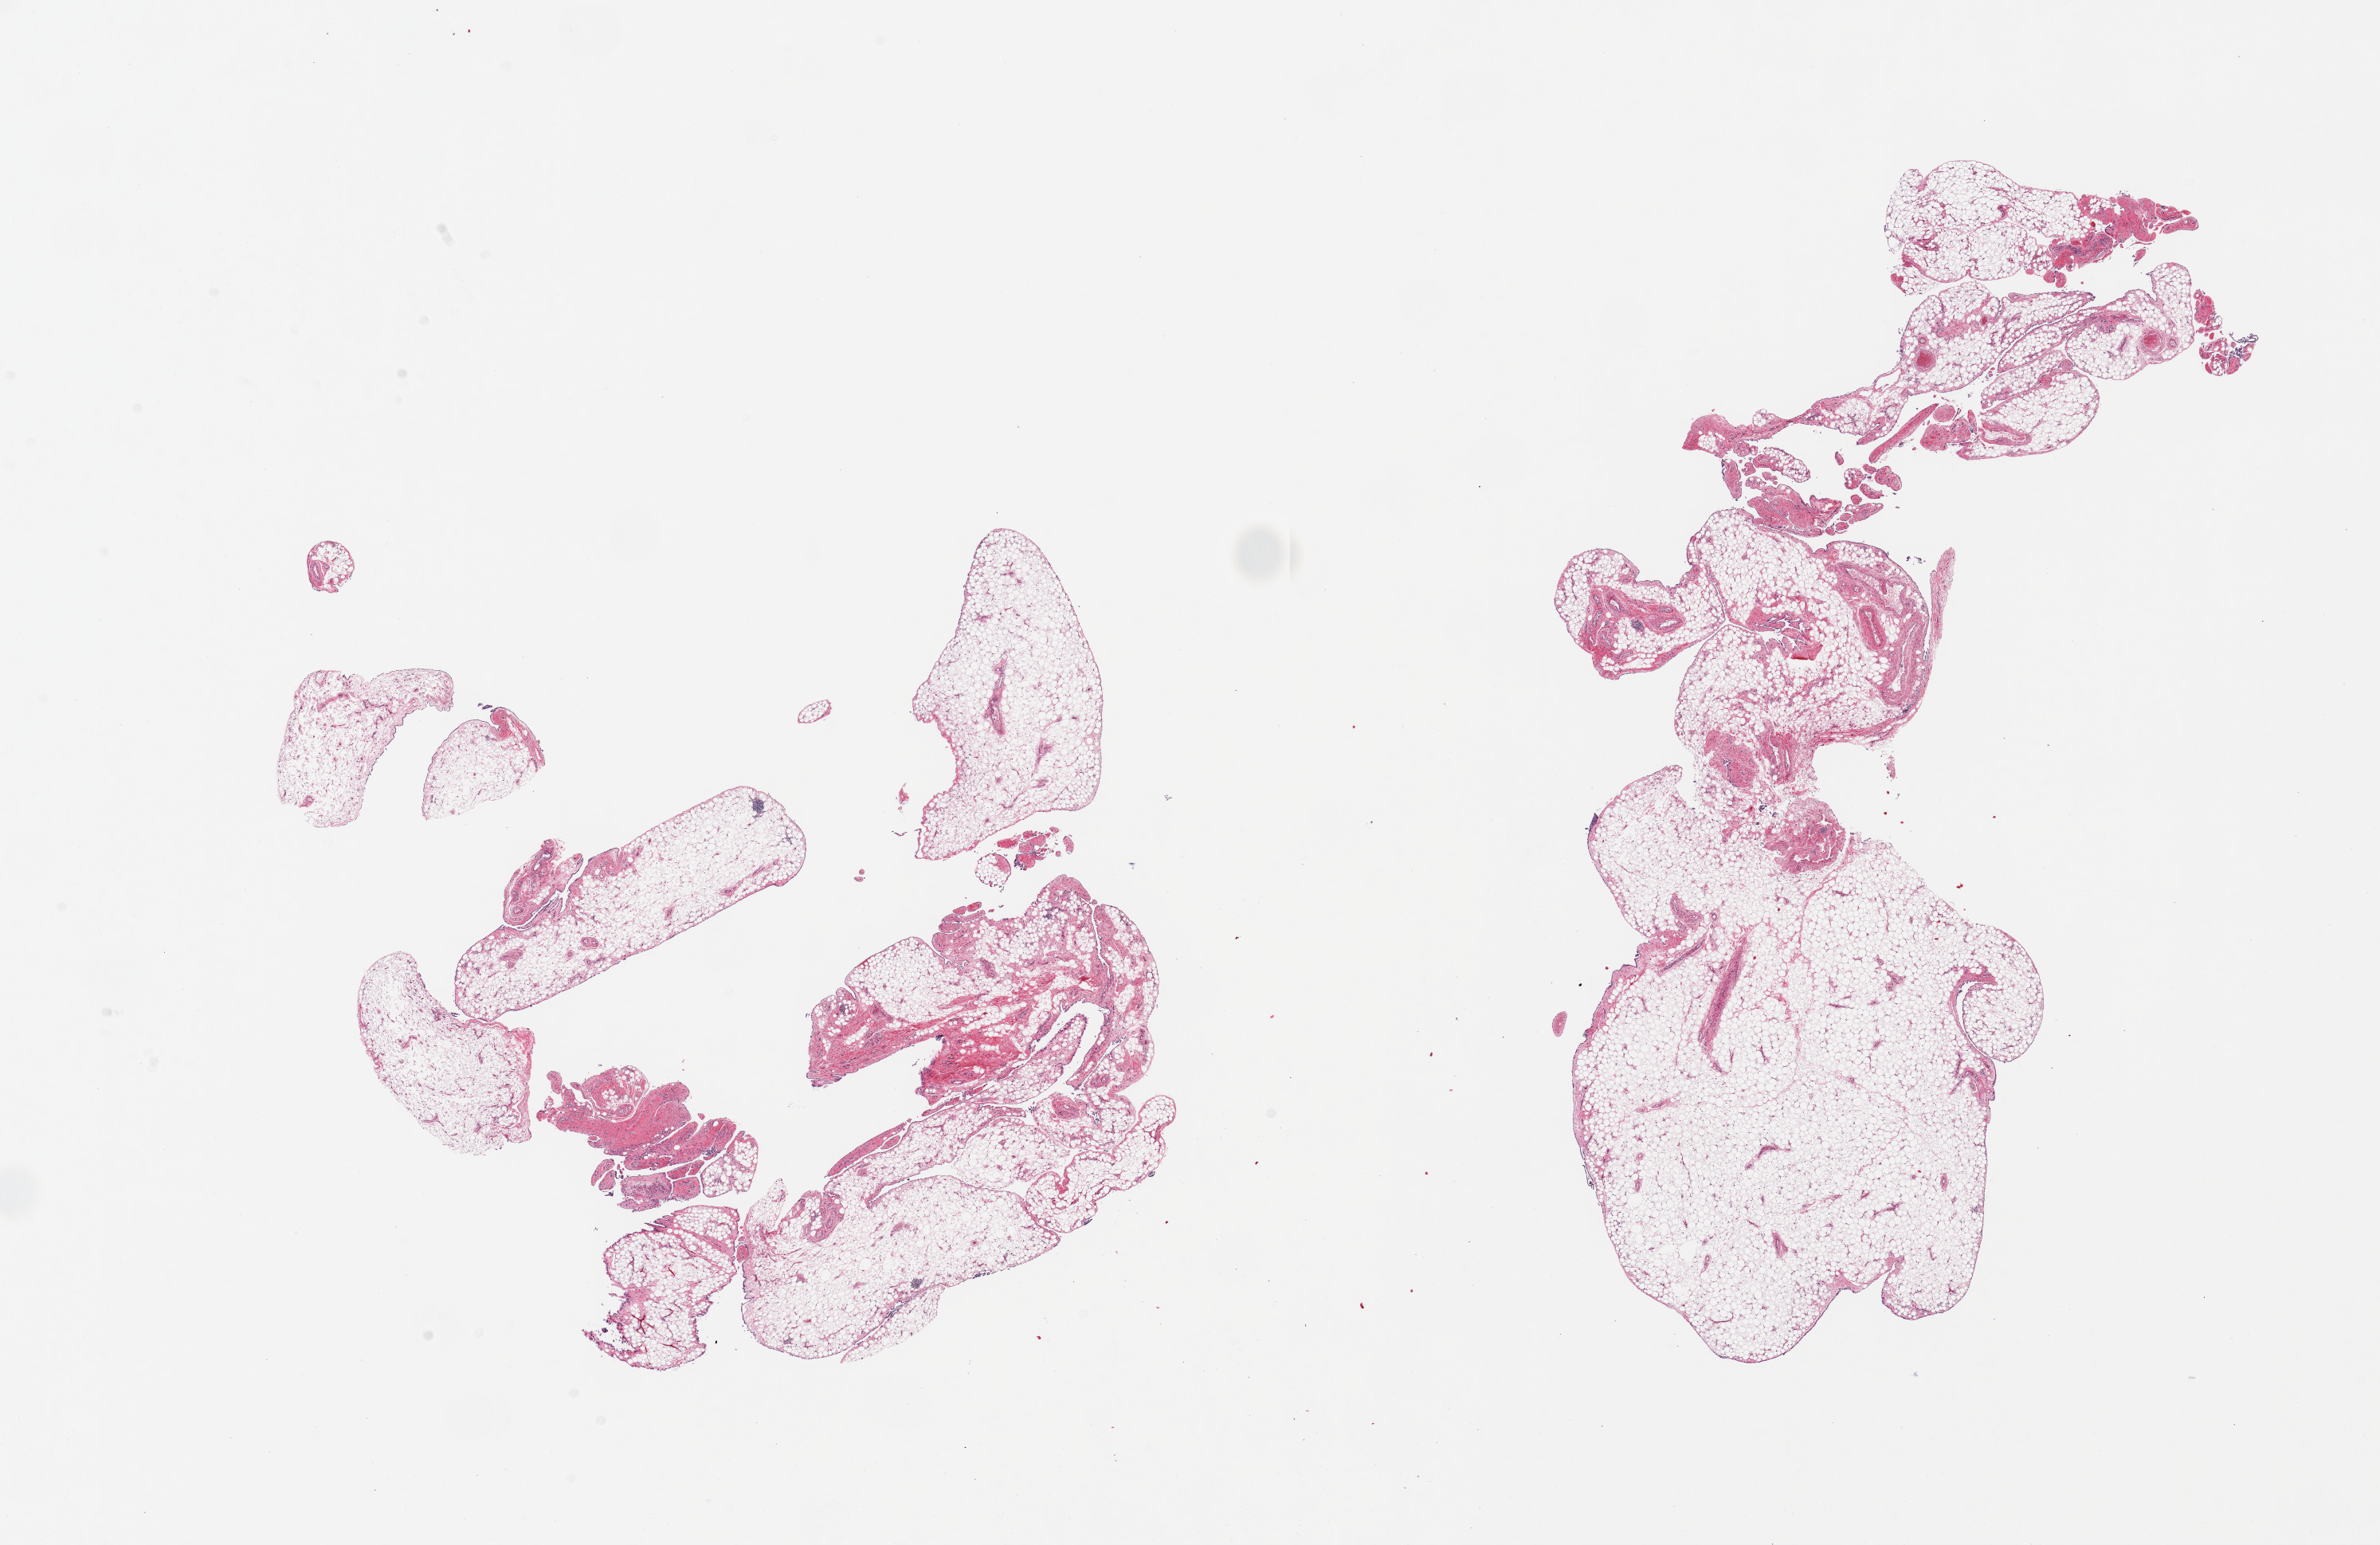
H&E whole-slide image, brightfield — a low-resolution overview of the entire scanned area, about 23.6 x 15.3 mm. PAXgene-fixed paraffin-embedded (PFPE) section. Section of omentum (target tissue). Tissue donor sample. Donor: female.
Pathologist's review note for this sample: 2 pieces; 10% fibrovascular content; well preserved mesothelial layer.